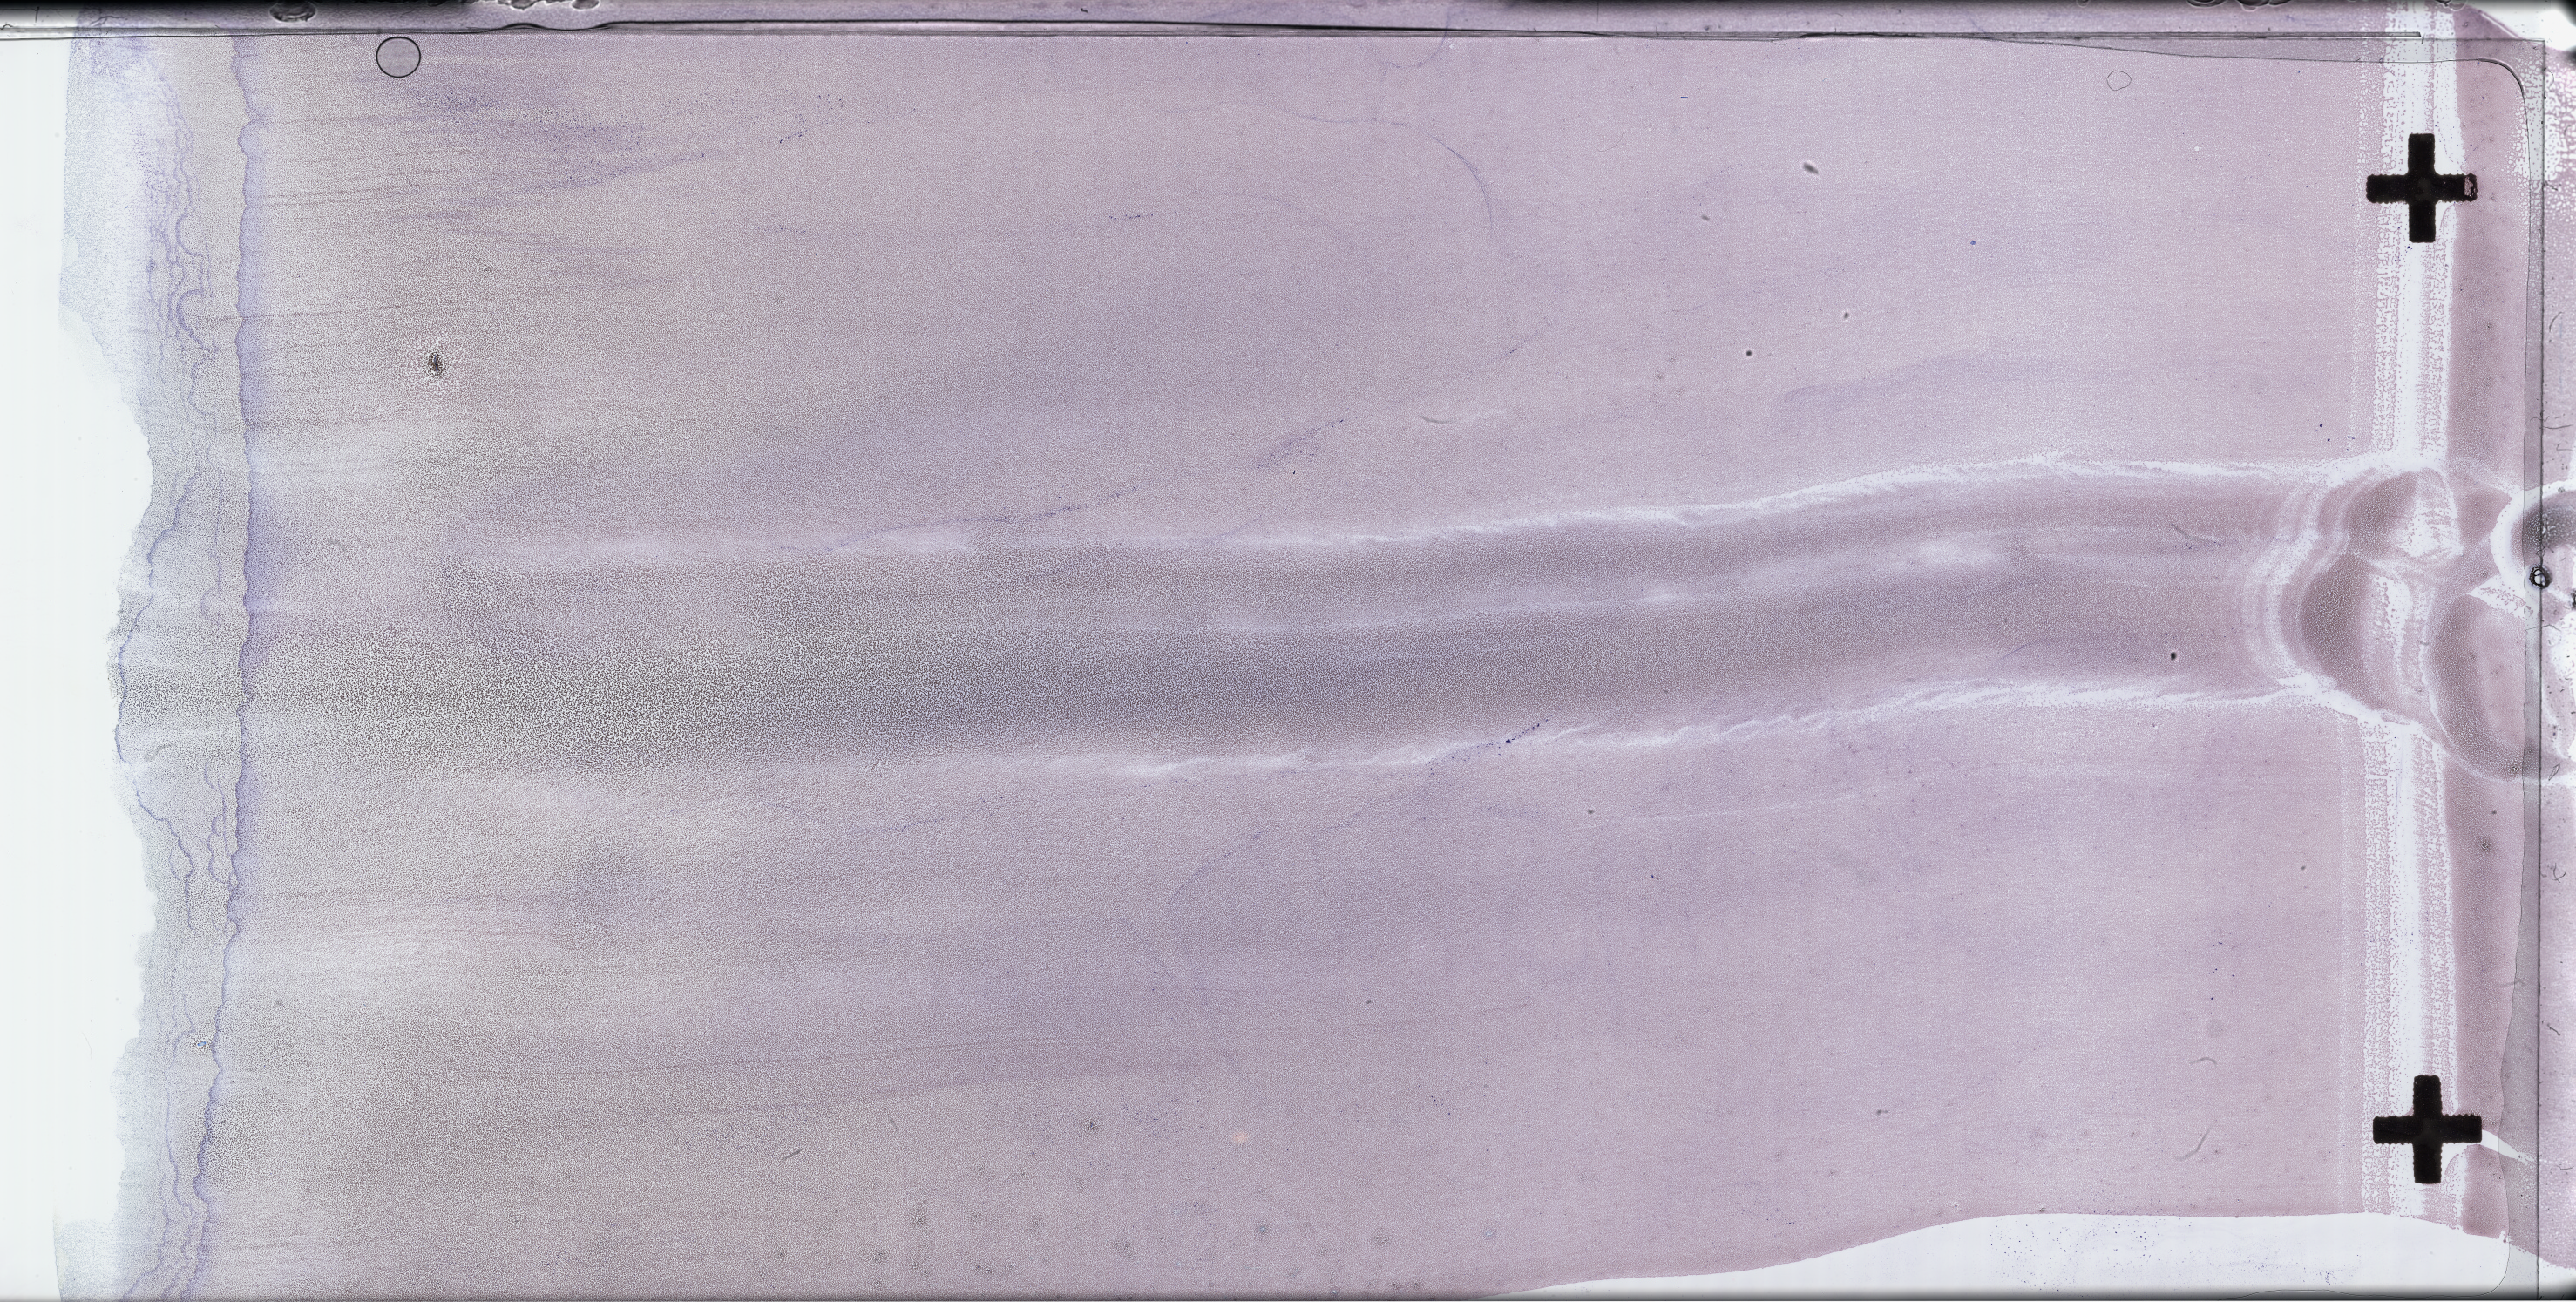
Wright-Giemsa-stained whole blood smear, whole-slide image, whole scanned area (about 47.7 x 24.1 mm) shown as a low-resolution overview. Smear from an EDTA sample. Collected at baseline (before treatment). Male patient.
• patient diagnosis: Plasma Cell Myeloma